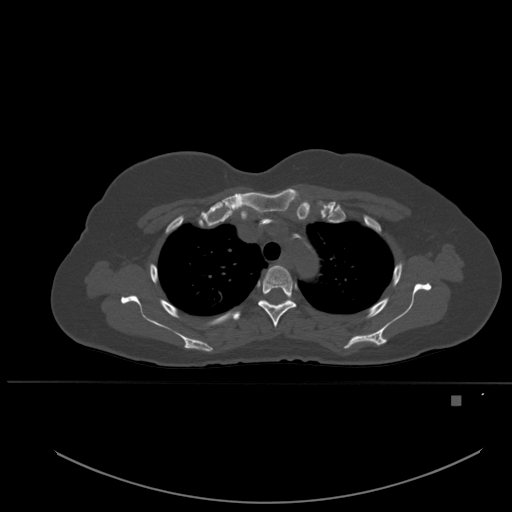
CT including the spine, one axial slice. Bone window (W 1800 / L 400 HU). 1.5 mm slice thickness. 512 × 512 image matrix, field of view 443 × 443 mm. Patient: female, 49 years. Case-level facts recorded for this patient, not image findings: primary cancer: breast; vertebrae with lytic lesions (as recorded): L3, T12, L4.
Structures marked on this image (semi-automatically segmented with operator editing):
- T3 vertebra: bounding box (x1, y1, x2, y2) in pixels: (258, 265, 296, 328)
- T4 vertebra: (266, 301, 272, 305)